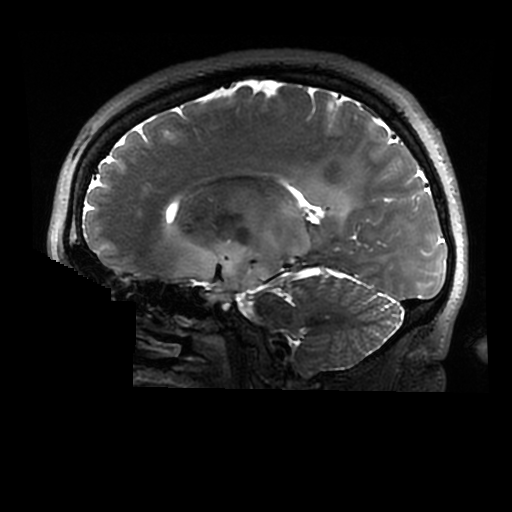
Brain MRI from a brain-tumour surgery series, one sagittal slice. Slice 177 of 320 in the series (ordered by position). 0.6 mm slice thickness. 512 × 512 image matrix. From the clinical record (not read from this slice): histopathology: Astrocytoma; WHO grade: 2; IDH mutation: yes.
Outlined on this slice (expert manual segmentation):
- tumour: bounding box [x1, y1, x2, y2] px = [189, 198, 351, 304]